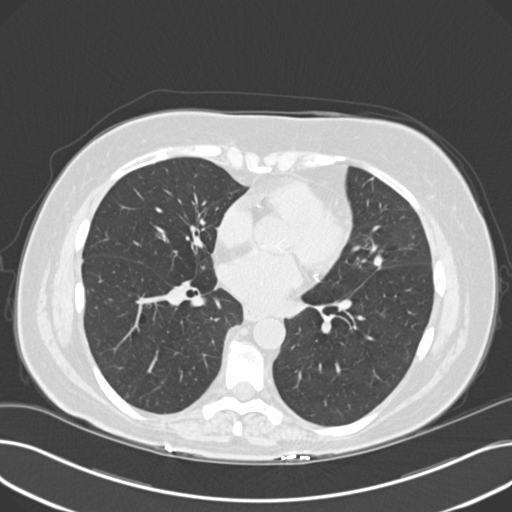
Low-dose screening chest CT, axial slice; third screening round (two years after baseline); lung window (W 1500 / L -600 HU); 2 mm slice thickness; standard (soft-tissue) reconstruction kernel (B30f); slice 114 of 203 in the series; 512 × 512 image matrix. Female participant, aged 60 years at enrolment. Current smoker at enrolment.
Expert-annotated lung lesion, bounding box <360,249,400,282> (left, top, right, bottom; pixels). The screening reader recorded 8 non-calcified nodules or masses ≥4 mm on this exam (right upper lobe, lingula, lingula, right middle lobe, right lower lobe, left lower lobe, left lower lobe, left lower lobe); which of them this box marks is not recorded. Official screen result: positive, other. Later outcome: lung cancer diagnosed 176 days after this screen — non-small cell carcinoma, left upper lobe, poorly differentiated (G3), stage IB (AJCC 6th edition), 7 mm at pathology.